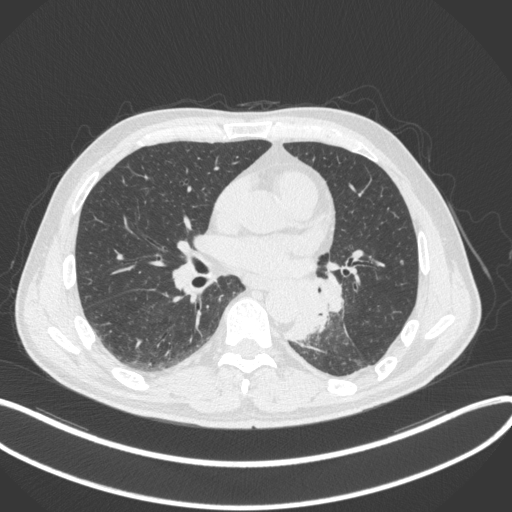
Chest CT, one axial slice; slice 160 of 328 in the series (ordered by position); lung window (W 1500 / L -600 HU); 1 mm slice thickness; 512 × 512 image matrix, field of view 400 × 400 mm. Male patient, age 59 years. Case-level facts recorded for this patient, not image findings: clinical TNM (as recorded): T2a N2 M0.
Structures marked on this image (bounding box drawn by a radiologist):
- lung tumour (recorded histology: squamous cell carcinoma): bounding box <283,274,350,344> (left, top, right, bottom; pixels)